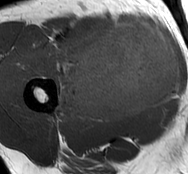
MRI of an extremity soft-tissue mass, one axial slice. Slice 40 of 93 in the series (ordered by position). MR volume resampled by the dataset authors to the PET/CT grid (not the native acquisition matrix). 188 × 174 image matrix. Male patient. Case-level facts recorded for this patient, not image findings: histological type: undifferentiated - pleiomorphic; grade: high; site of the primary tumour: right thigh.
Structures marked on this image (expert contour drawn on MRI and transferred to this co-registered scan by the dataset authors):
- gross tumour volume including surrounding oedema: box from (x=56, y=19) to (x=181, y=123) px
- gross tumour volume (mass): (x=70, y=21)–(x=180, y=118)